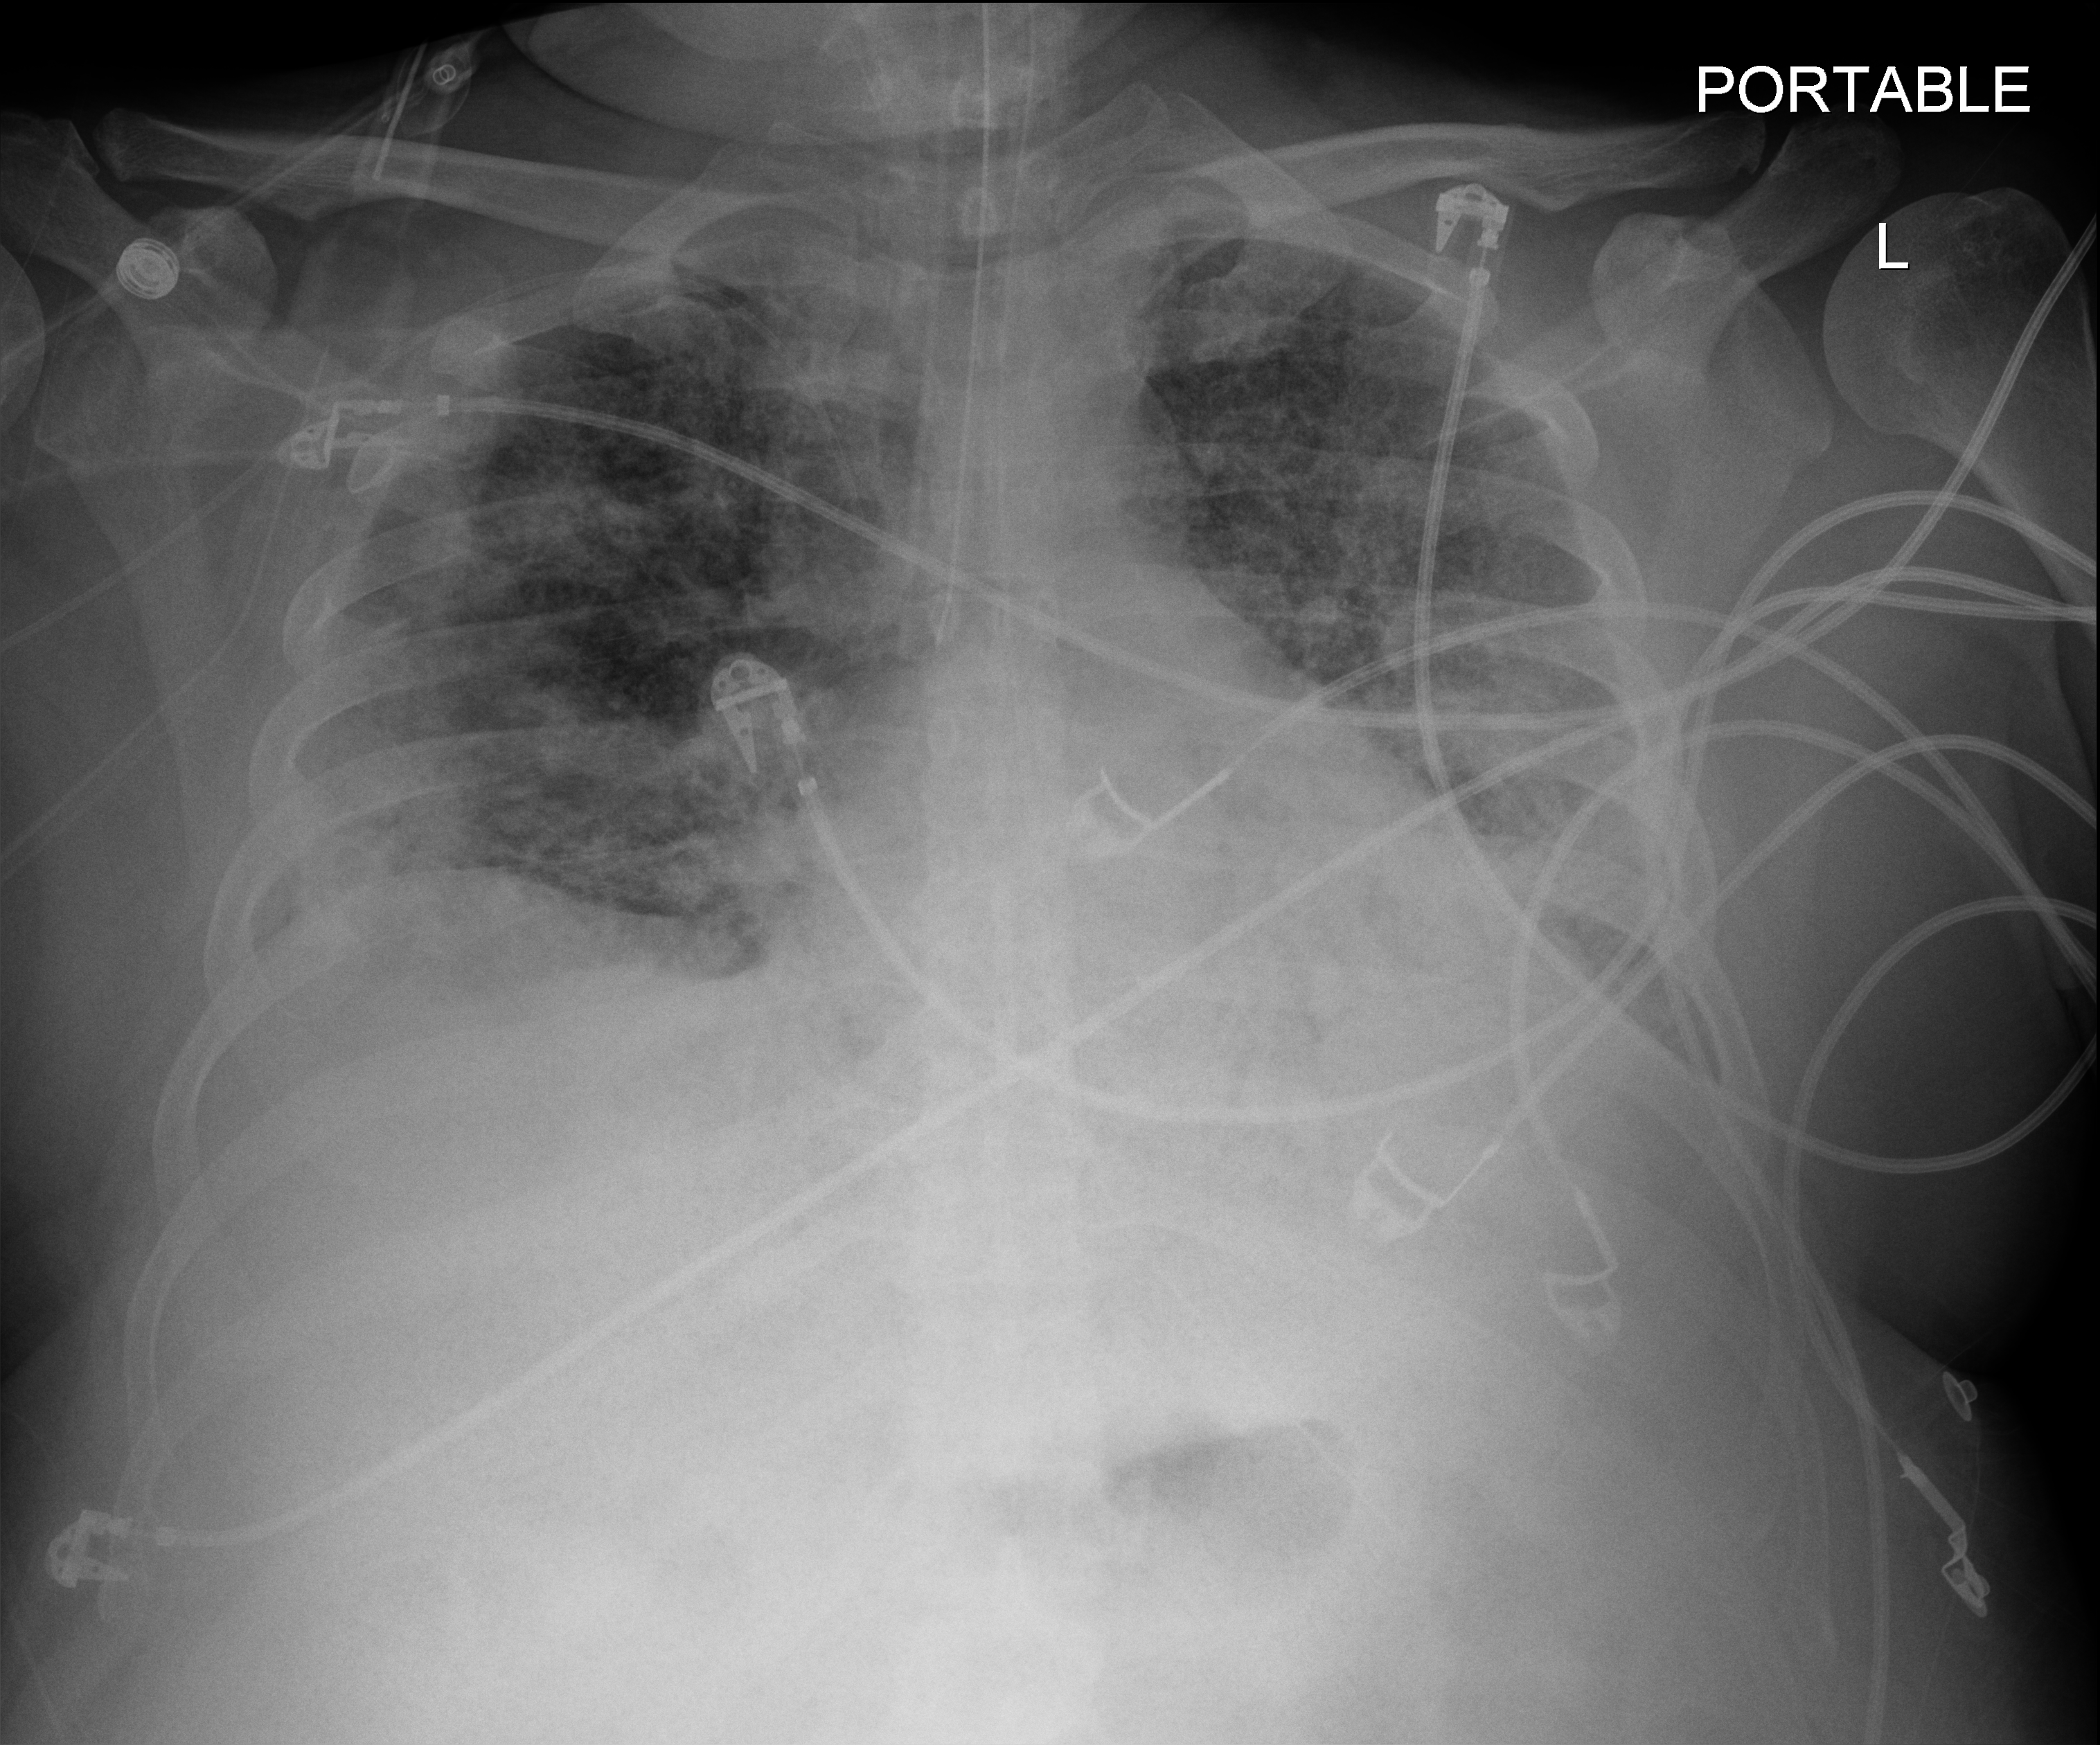
Bedside chest radiograph (digital radiography), anteroposterior (AP) projection. Male patient hospitalised with COVID-19, age 18–59 years.
From the hospital-stay record, not from the radiograph (when in the stay this image was taken is not recorded):
- admitted to intensive care during this hospital stay: yes
- mechanically ventilated during this hospital stay: yes